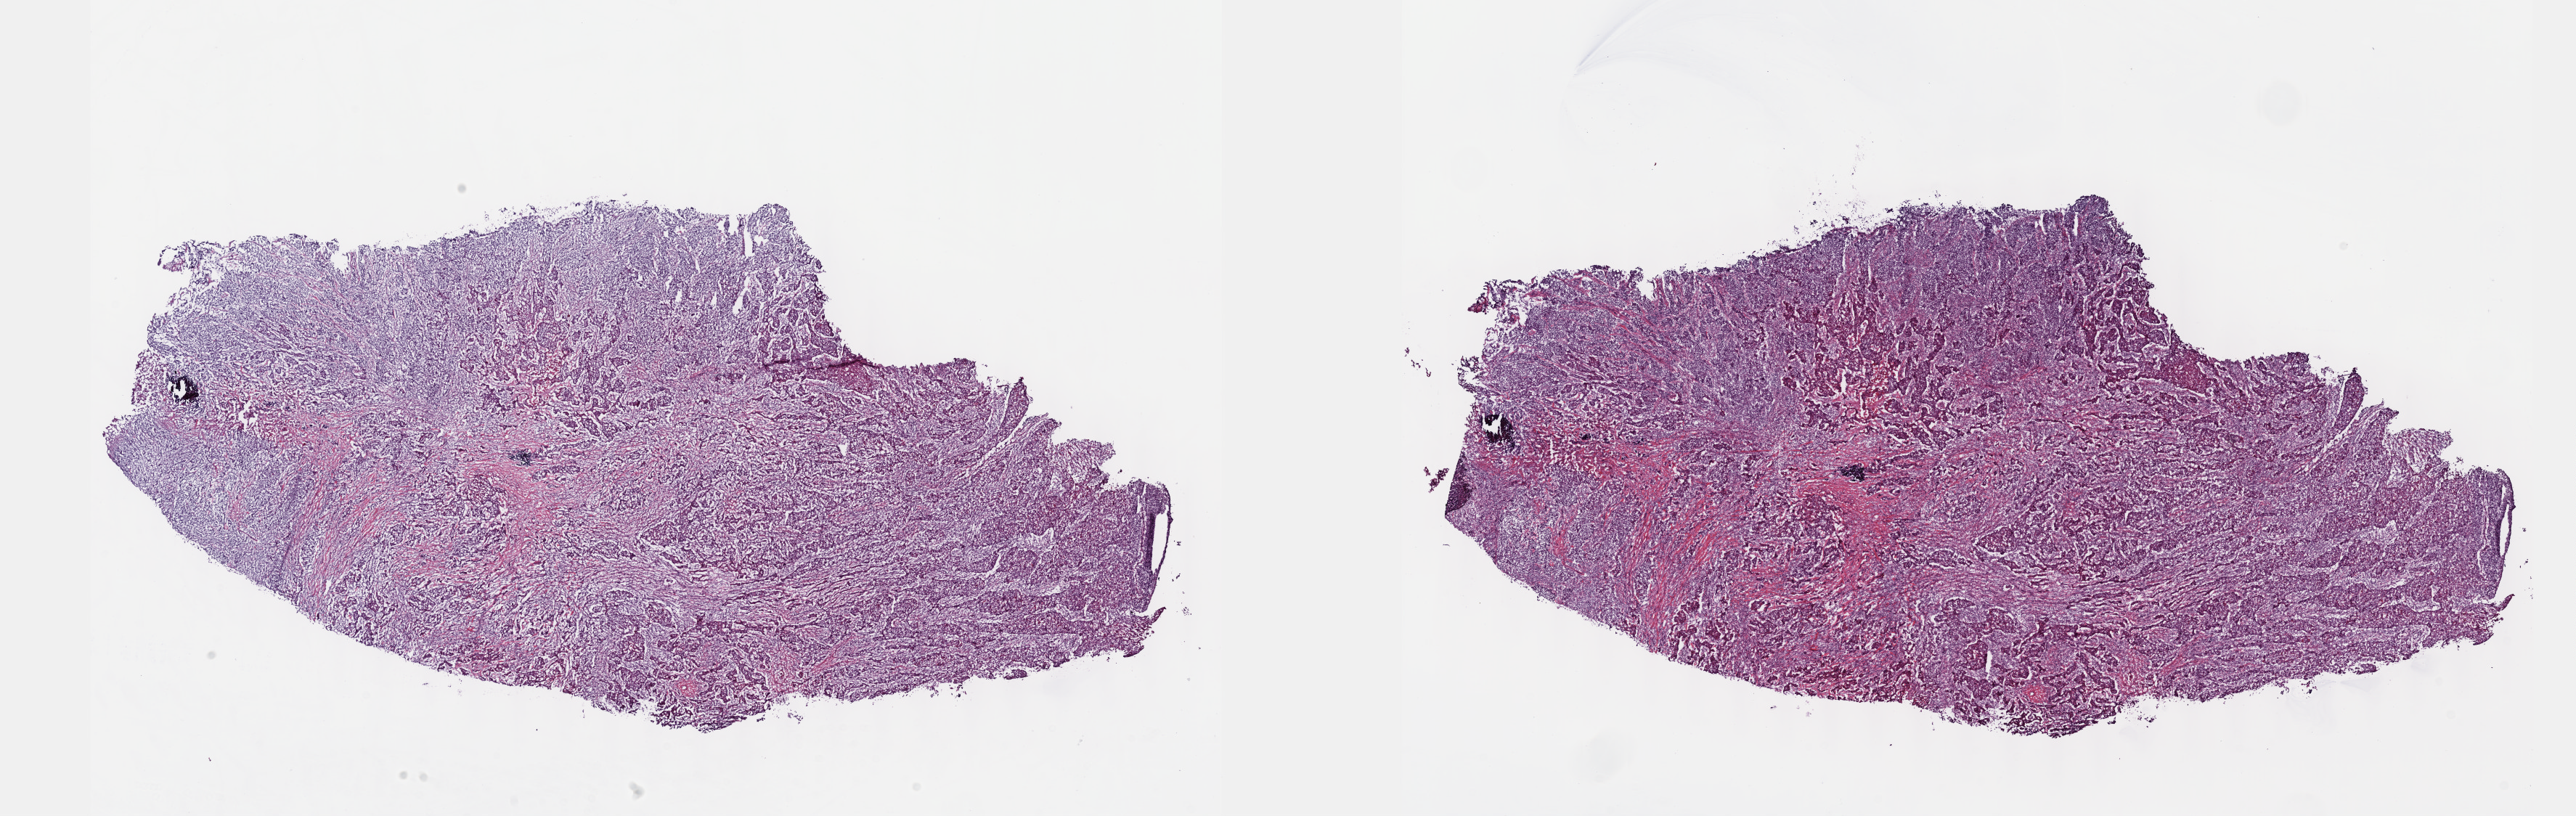
Whole-slide histology image, Hematoxylin and eosin (H&E) stained, whole scanned area (about 28.7 x 9.1 mm) shown as a low-resolution overview. Frozen section from the top of the tissue portion. Bladder, primary tumour sample. Male, age 56 years at initial diagnosis. Histologic grade: high grade. Slide review estimates, as recorded: tumour cells 50%, tumour nuclei 60%, normal cells 0%, stromal cells 50%, necrosis 0%. Inflammatory infiltration, as recorded: lymphocyte infiltration 0%, monocyte infiltration 0%, neutrophil infiltration 0%.
• lymph nodes positive (case pathology): 0 of 15 examined
• AJCC pathologic stage: III (6th edition)
• histologic diagnosis: Transitional cell carcinoma